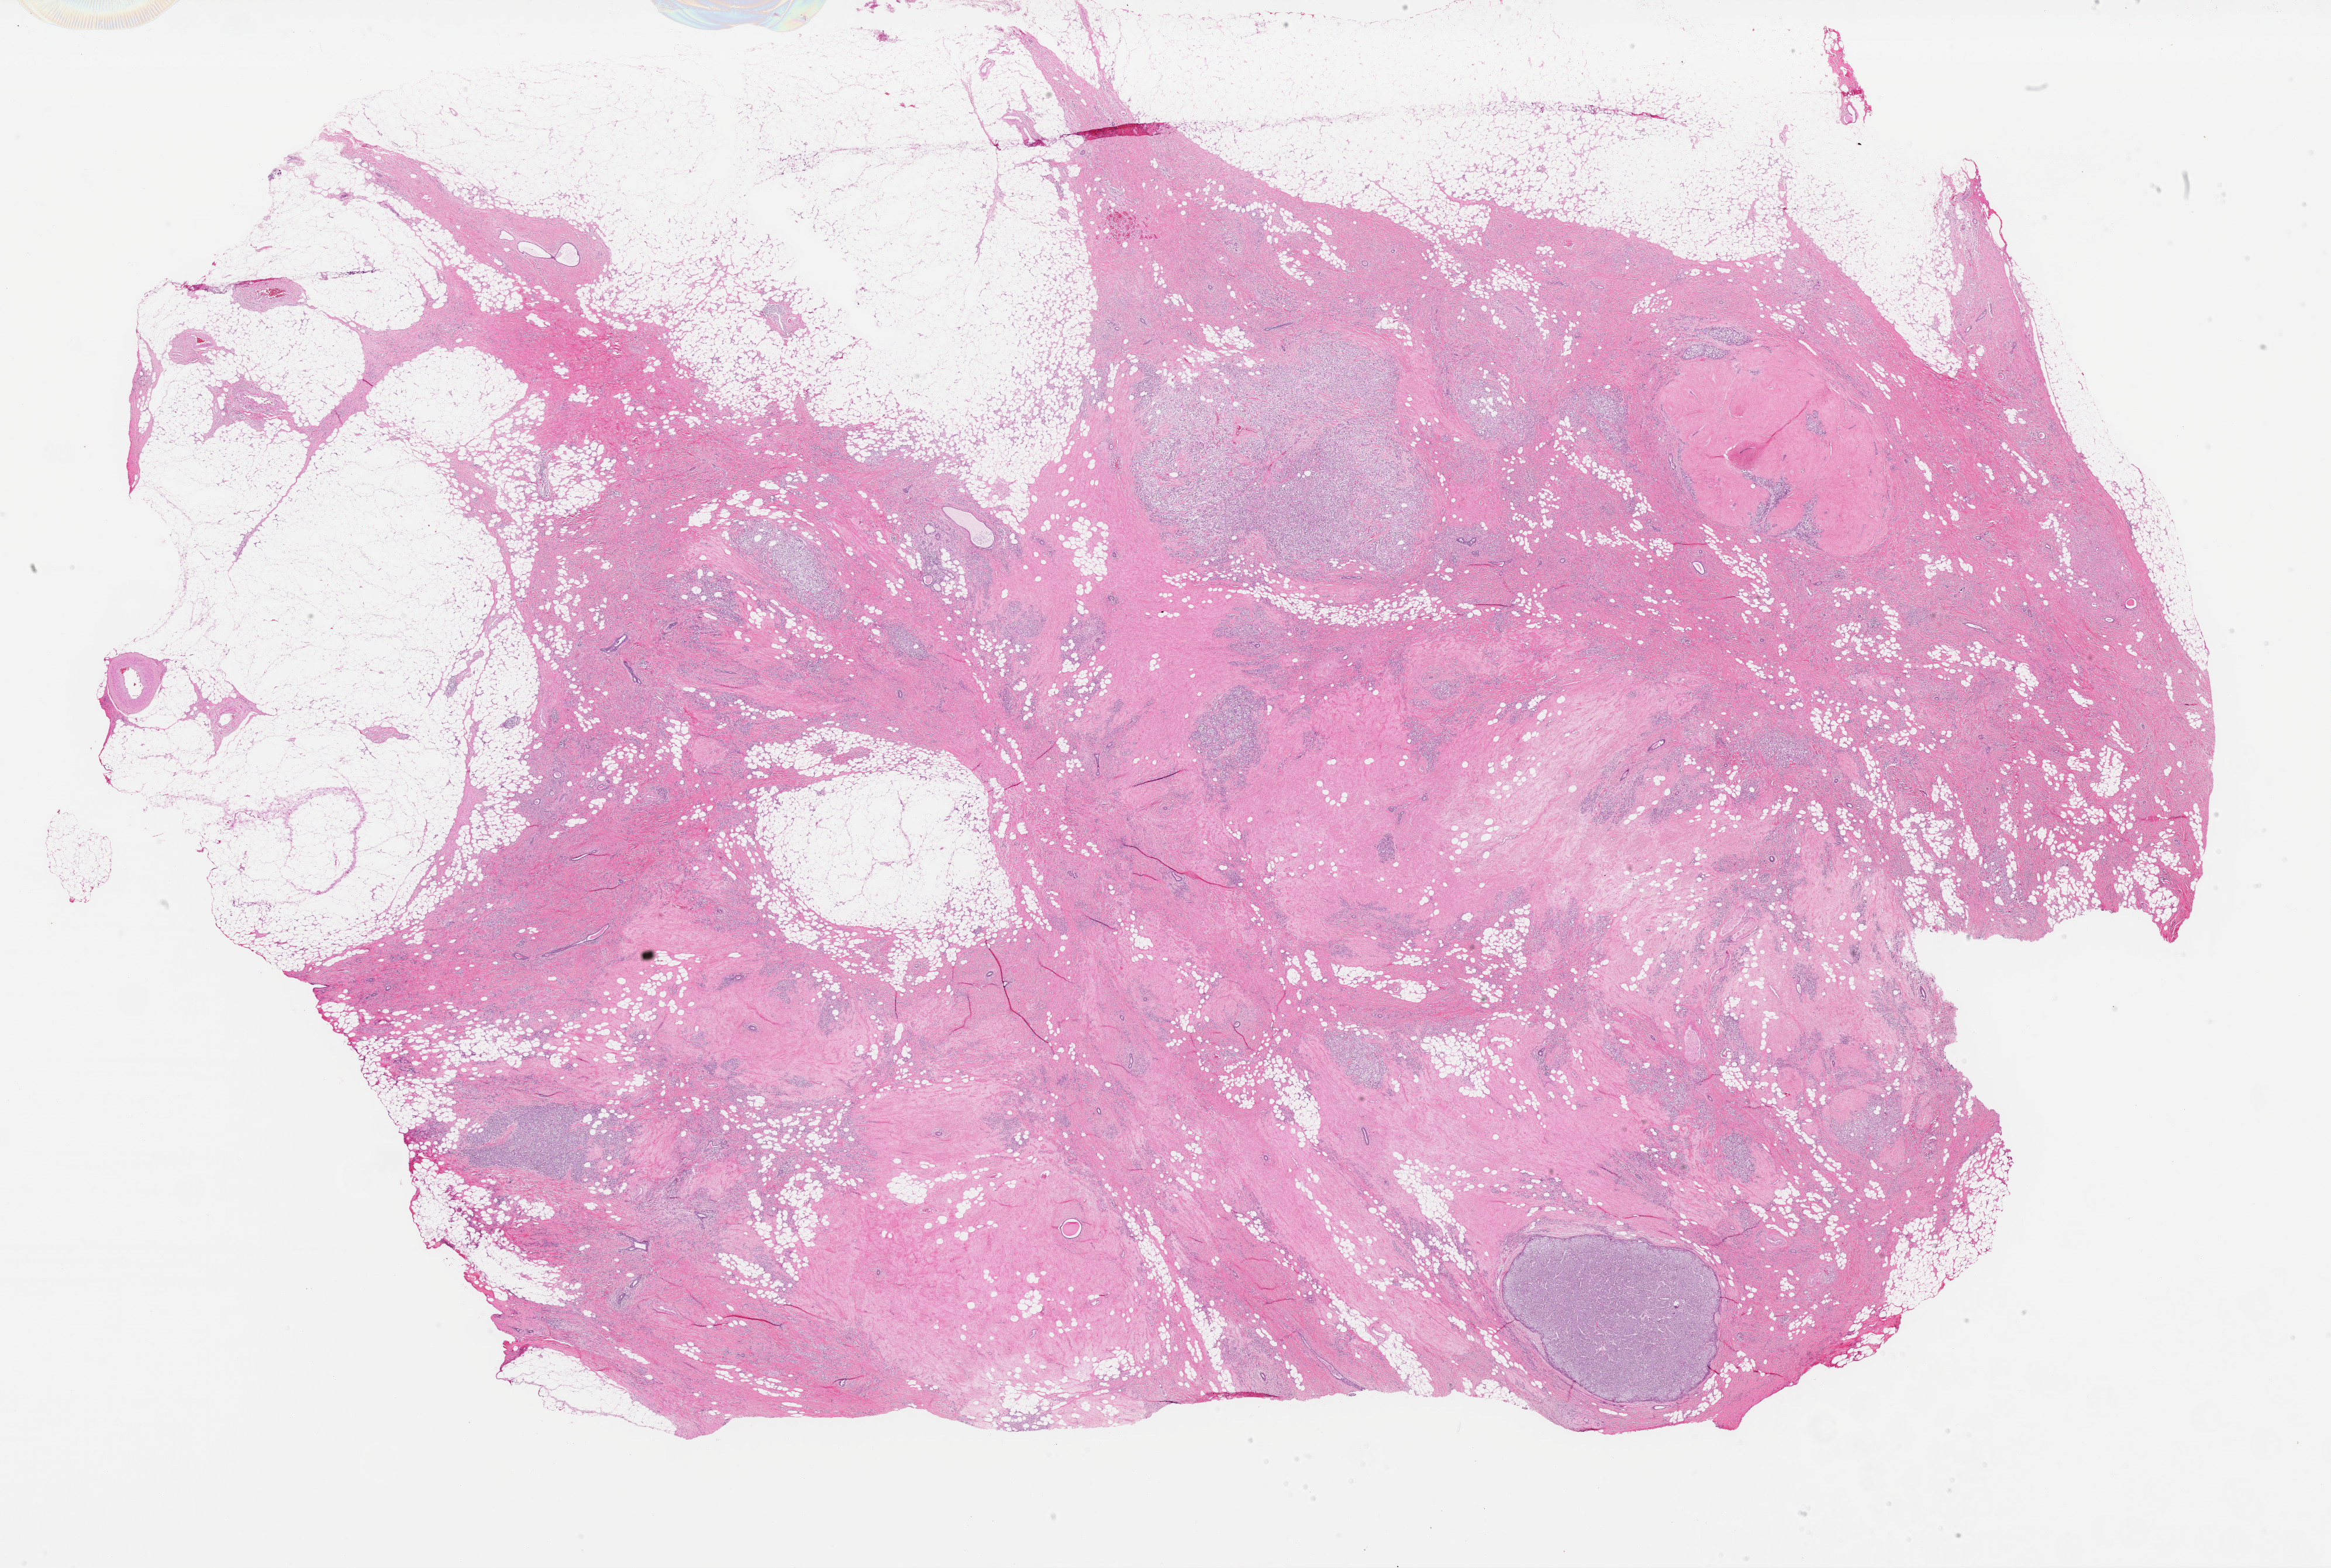
Hematoxylin and eosin (H&E) stained whole-slide image, shown as a low-resolution overview of the whole scanned area (about 31.5 x 21.2 mm, acquisition: 40x scan), formalin-fixed paraffin-embedded (FFPE) diagnostic section, breast, primary tumour sample. Female patient; age at initial diagnosis 62 years.
Lymph nodes positive (case pathology): 0 of 28 examined. Laterality: right. AJCC pathologic stage: IIA (5th edition). Histologic diagnosis: Lobular carcinoma, NOS.